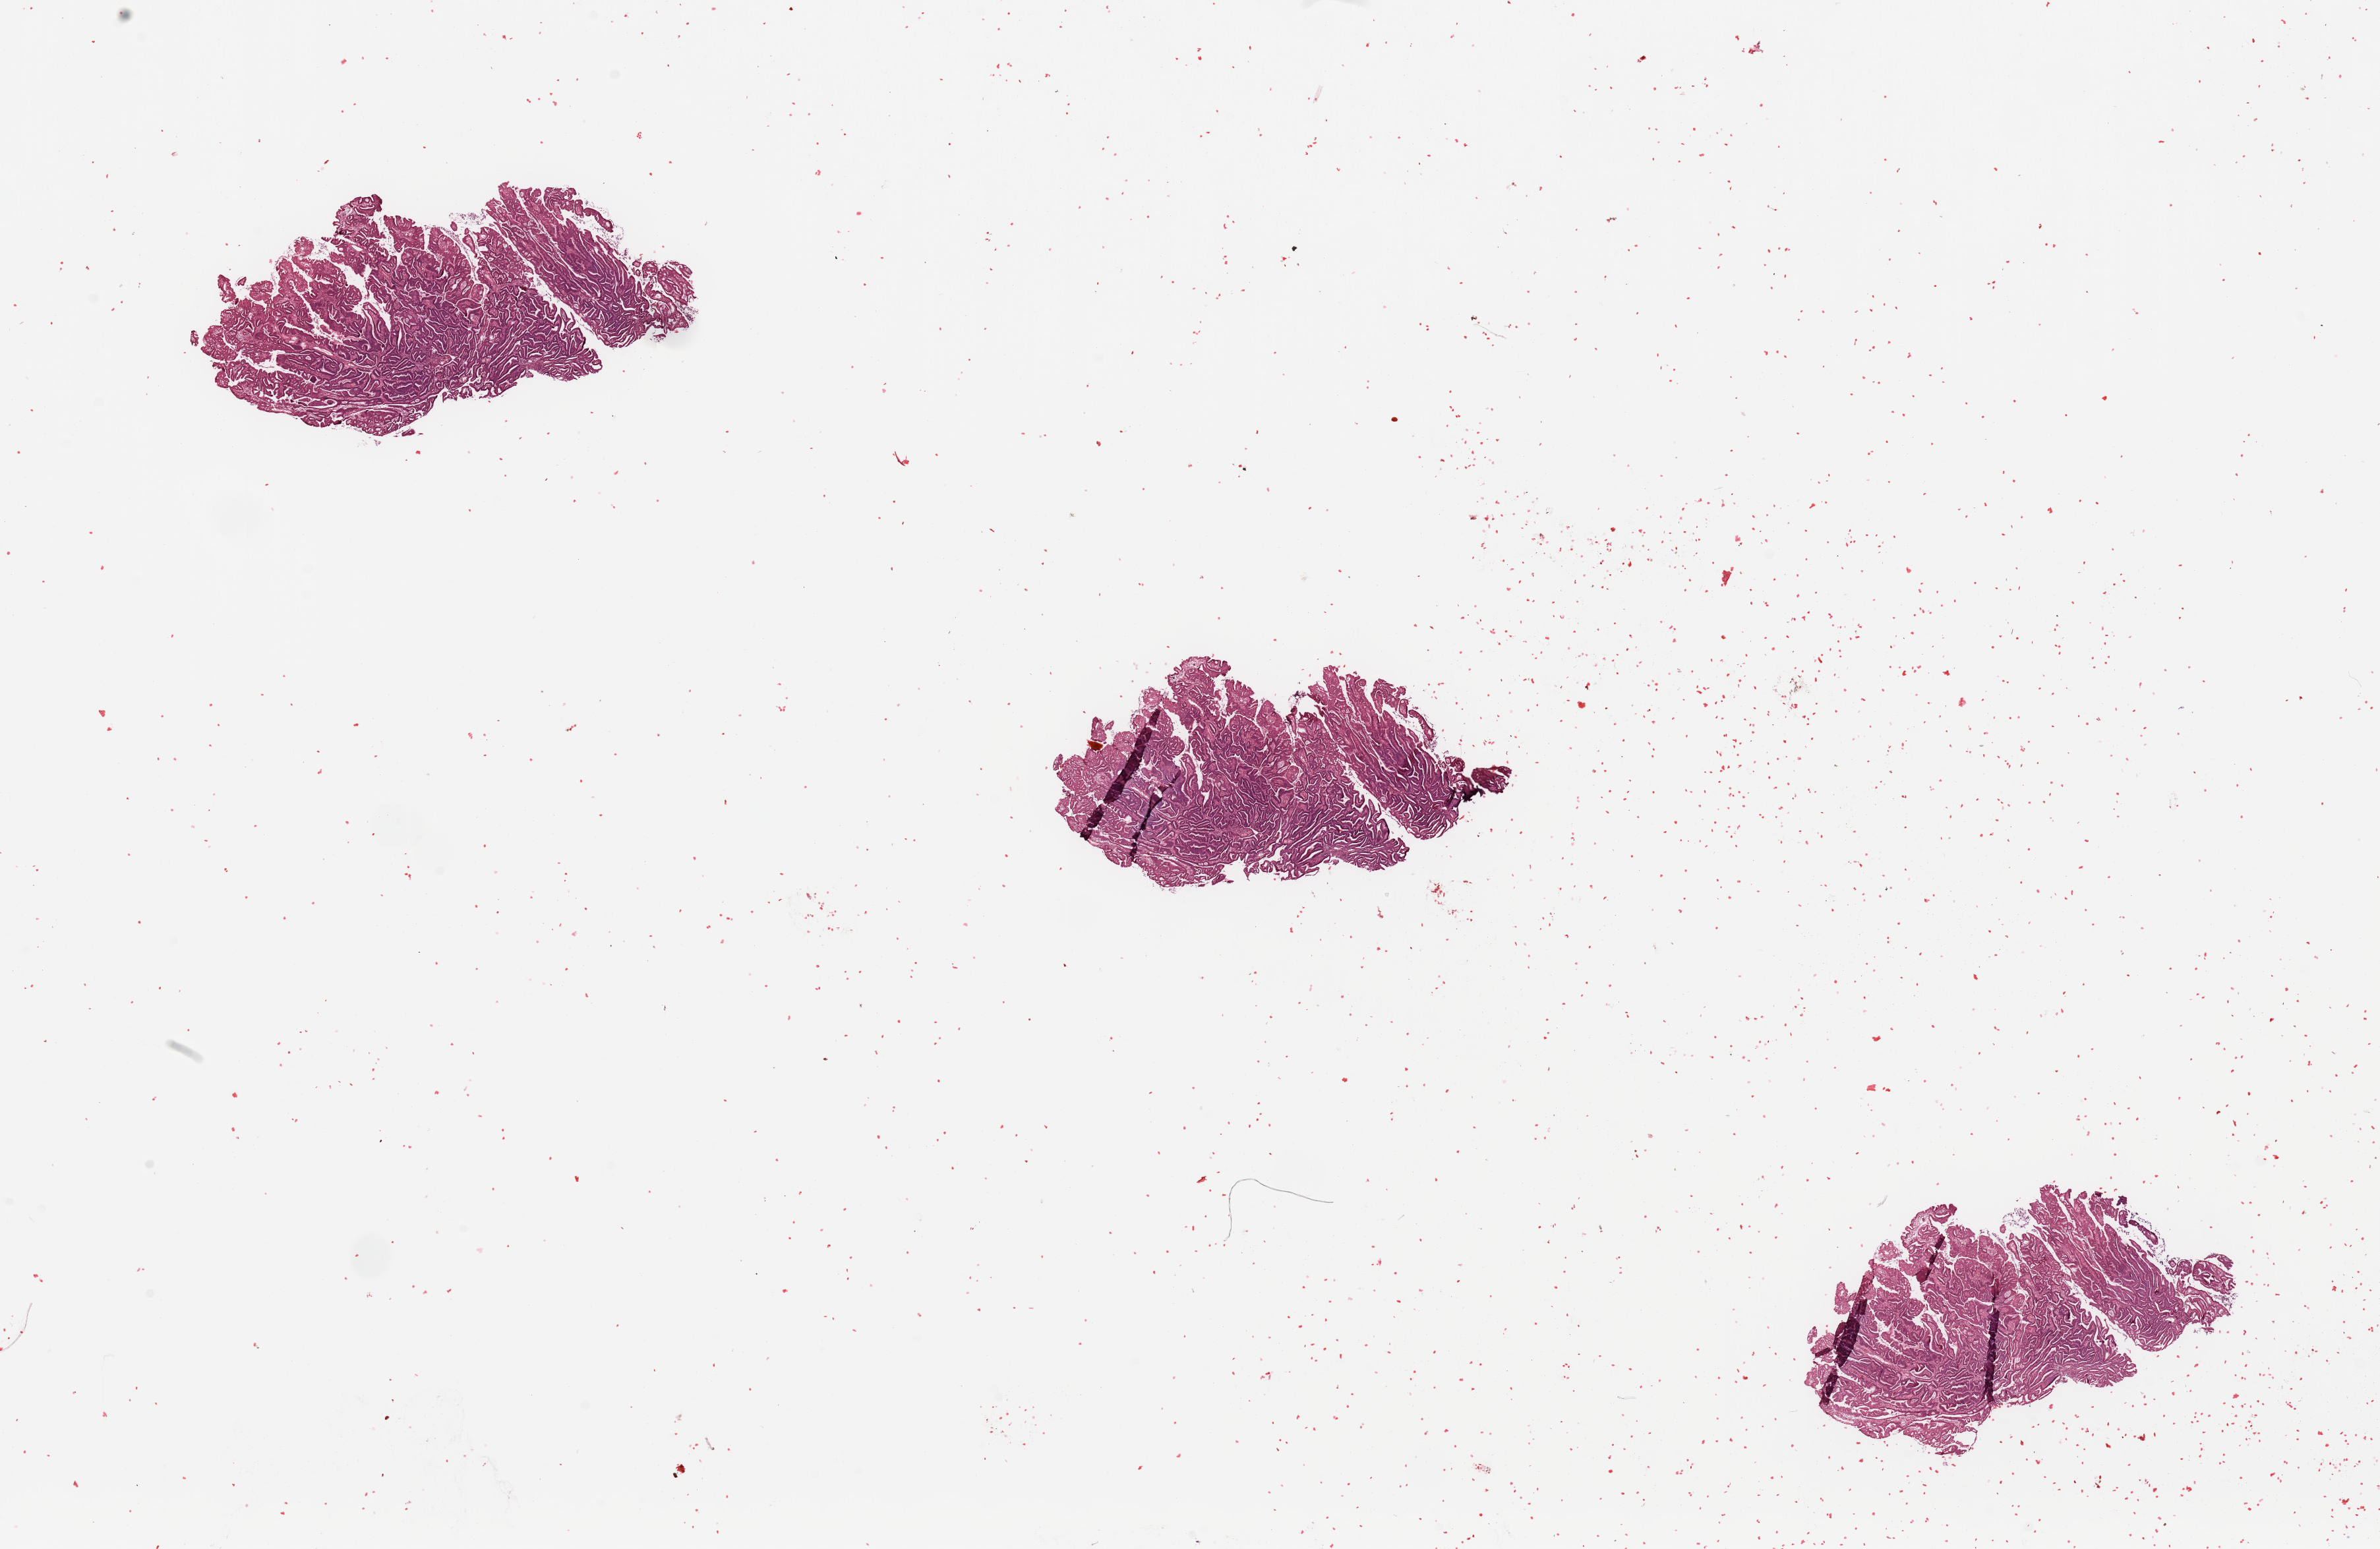
Hematoxylin and eosin (H&E) stained whole-slide image, shown as a low-resolution overview of the whole scanned area (about 28.5 x 18.6 mm). Tumour tissue sample, uterus. 69-year-old female patient. Histologic grade: G1 (well differentiated).
Histologic diagnosis: Endometrioid adenocarcinoma, NOS. Primary tumour site (as recorded): anterior endometrium. AJCC pathologic stage: I.